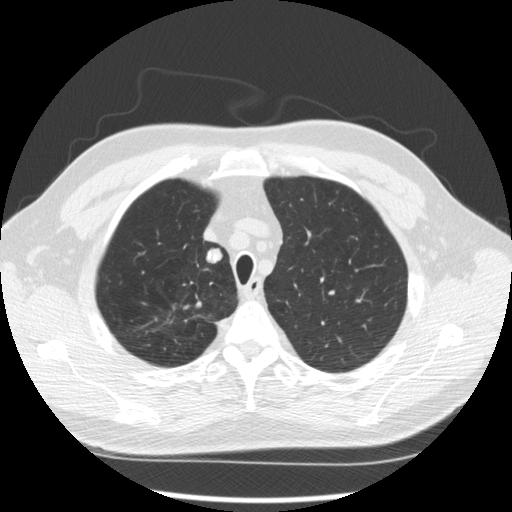
Chest CT (low-dose screening protocol), one axial image, second screening round (one year after baseline), lung window (W 1500 / L -600 HU), 2.5 mm slice thickness, 120 kVp, slice 50 of 289 in the series, 512 × 512 image matrix, field of view 360 × 360 mm. Male, age 64 years at enrolment. Former smoker at enrolment.
2 expert reader's lesion annotations on this slice (largest first), bounding box [x1, y1, x2, y2] px = [167, 296, 222, 332]; [190, 245, 226, 273]. The screening reader recorded 3 non-calcified nodules or masses ≥4 mm on this exam (right upper lobe, right upper lobe, right upper lobe); which of them these boxes mark is not recorded. Official screen result: positive, other. Lung cancer was diagnosed 411 days after this screen (after the third annual screen): adenocarcinoma, NOS, right upper lobe, moderately differentiated (G2), stage IA (AJCC 6th edition), 14 mm at pathology.